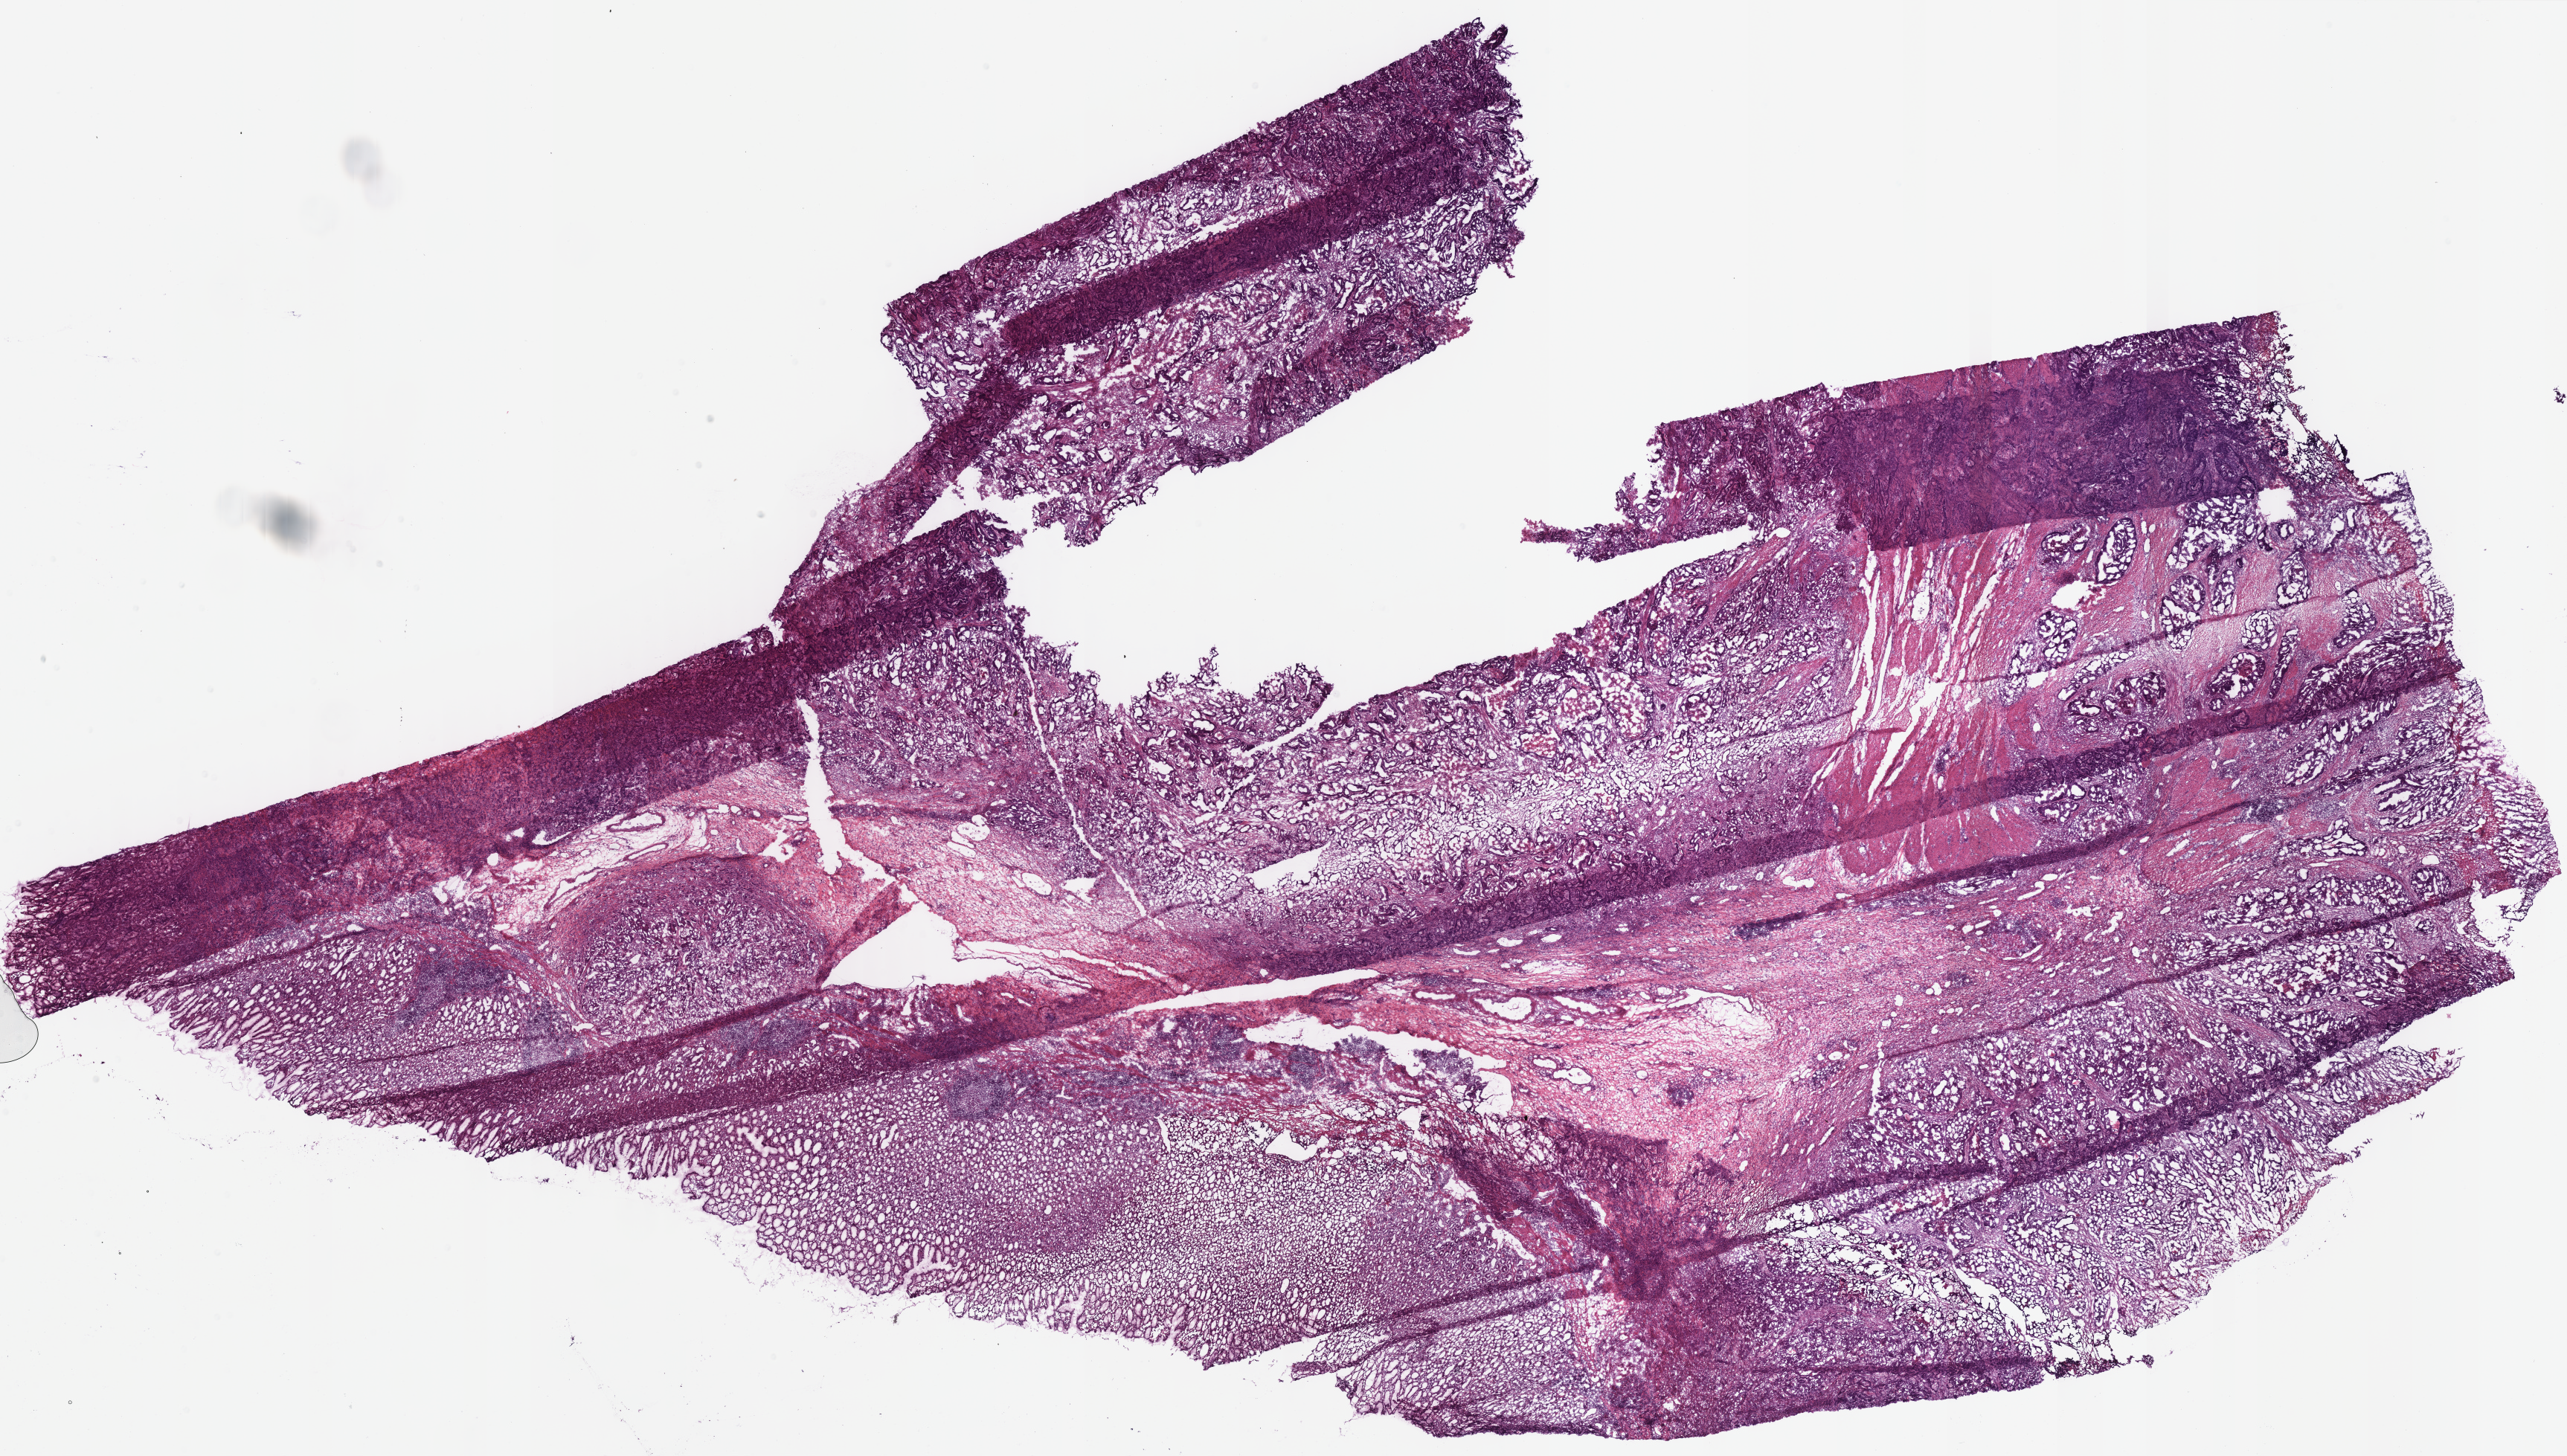
Hematoxylin and eosin (H&E) stained whole-slide image — whole scanned area (about 27.2 x 15.4 mm) shown as a low-resolution overview. Frozen section. Sample: primary tumour, stomach. Male patient; age at initial diagnosis 45 years. Histologic grade: G2 (moderately differentiated). Pathologist review of this section (percent, as recorded): tumour cells 68%, tumour nuclei 65%, normal cells 20%, stromal cells 2%, necrosis 10%. Infiltration values recorded for this section: lymphocyte infiltration 15%, monocyte infiltration 0%, neutrophil infiltration 0%.
* TNM: T4b N2 M1
* lymph nodes positive (case pathology): 3 of 10 examined
* AJCC pathologic stage: IV (7th edition)
* histologic diagnosis: Tubular adenocarcinoma (gastric antrum)